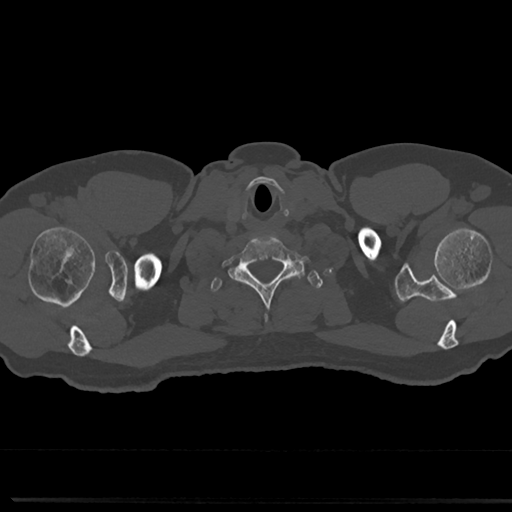
CT including the spine, one axial slice. Position 699 of 817 along the scan axis. 120 kVp. Bone window (W 1800 / L 400 HU). 0.5 mm slice thickness. 512 × 512 image matrix, field of view 355 × 355 mm. Male patient, age 61 years. Case-level facts recorded for this patient, not image findings: primary cancer: prostate.
Outlined on this slice (semi-automatically segmented with operator editing):
- T1 vertebra: bounding box (x1, y1, x2, y2) in pixels: (209, 268, 319, 296)